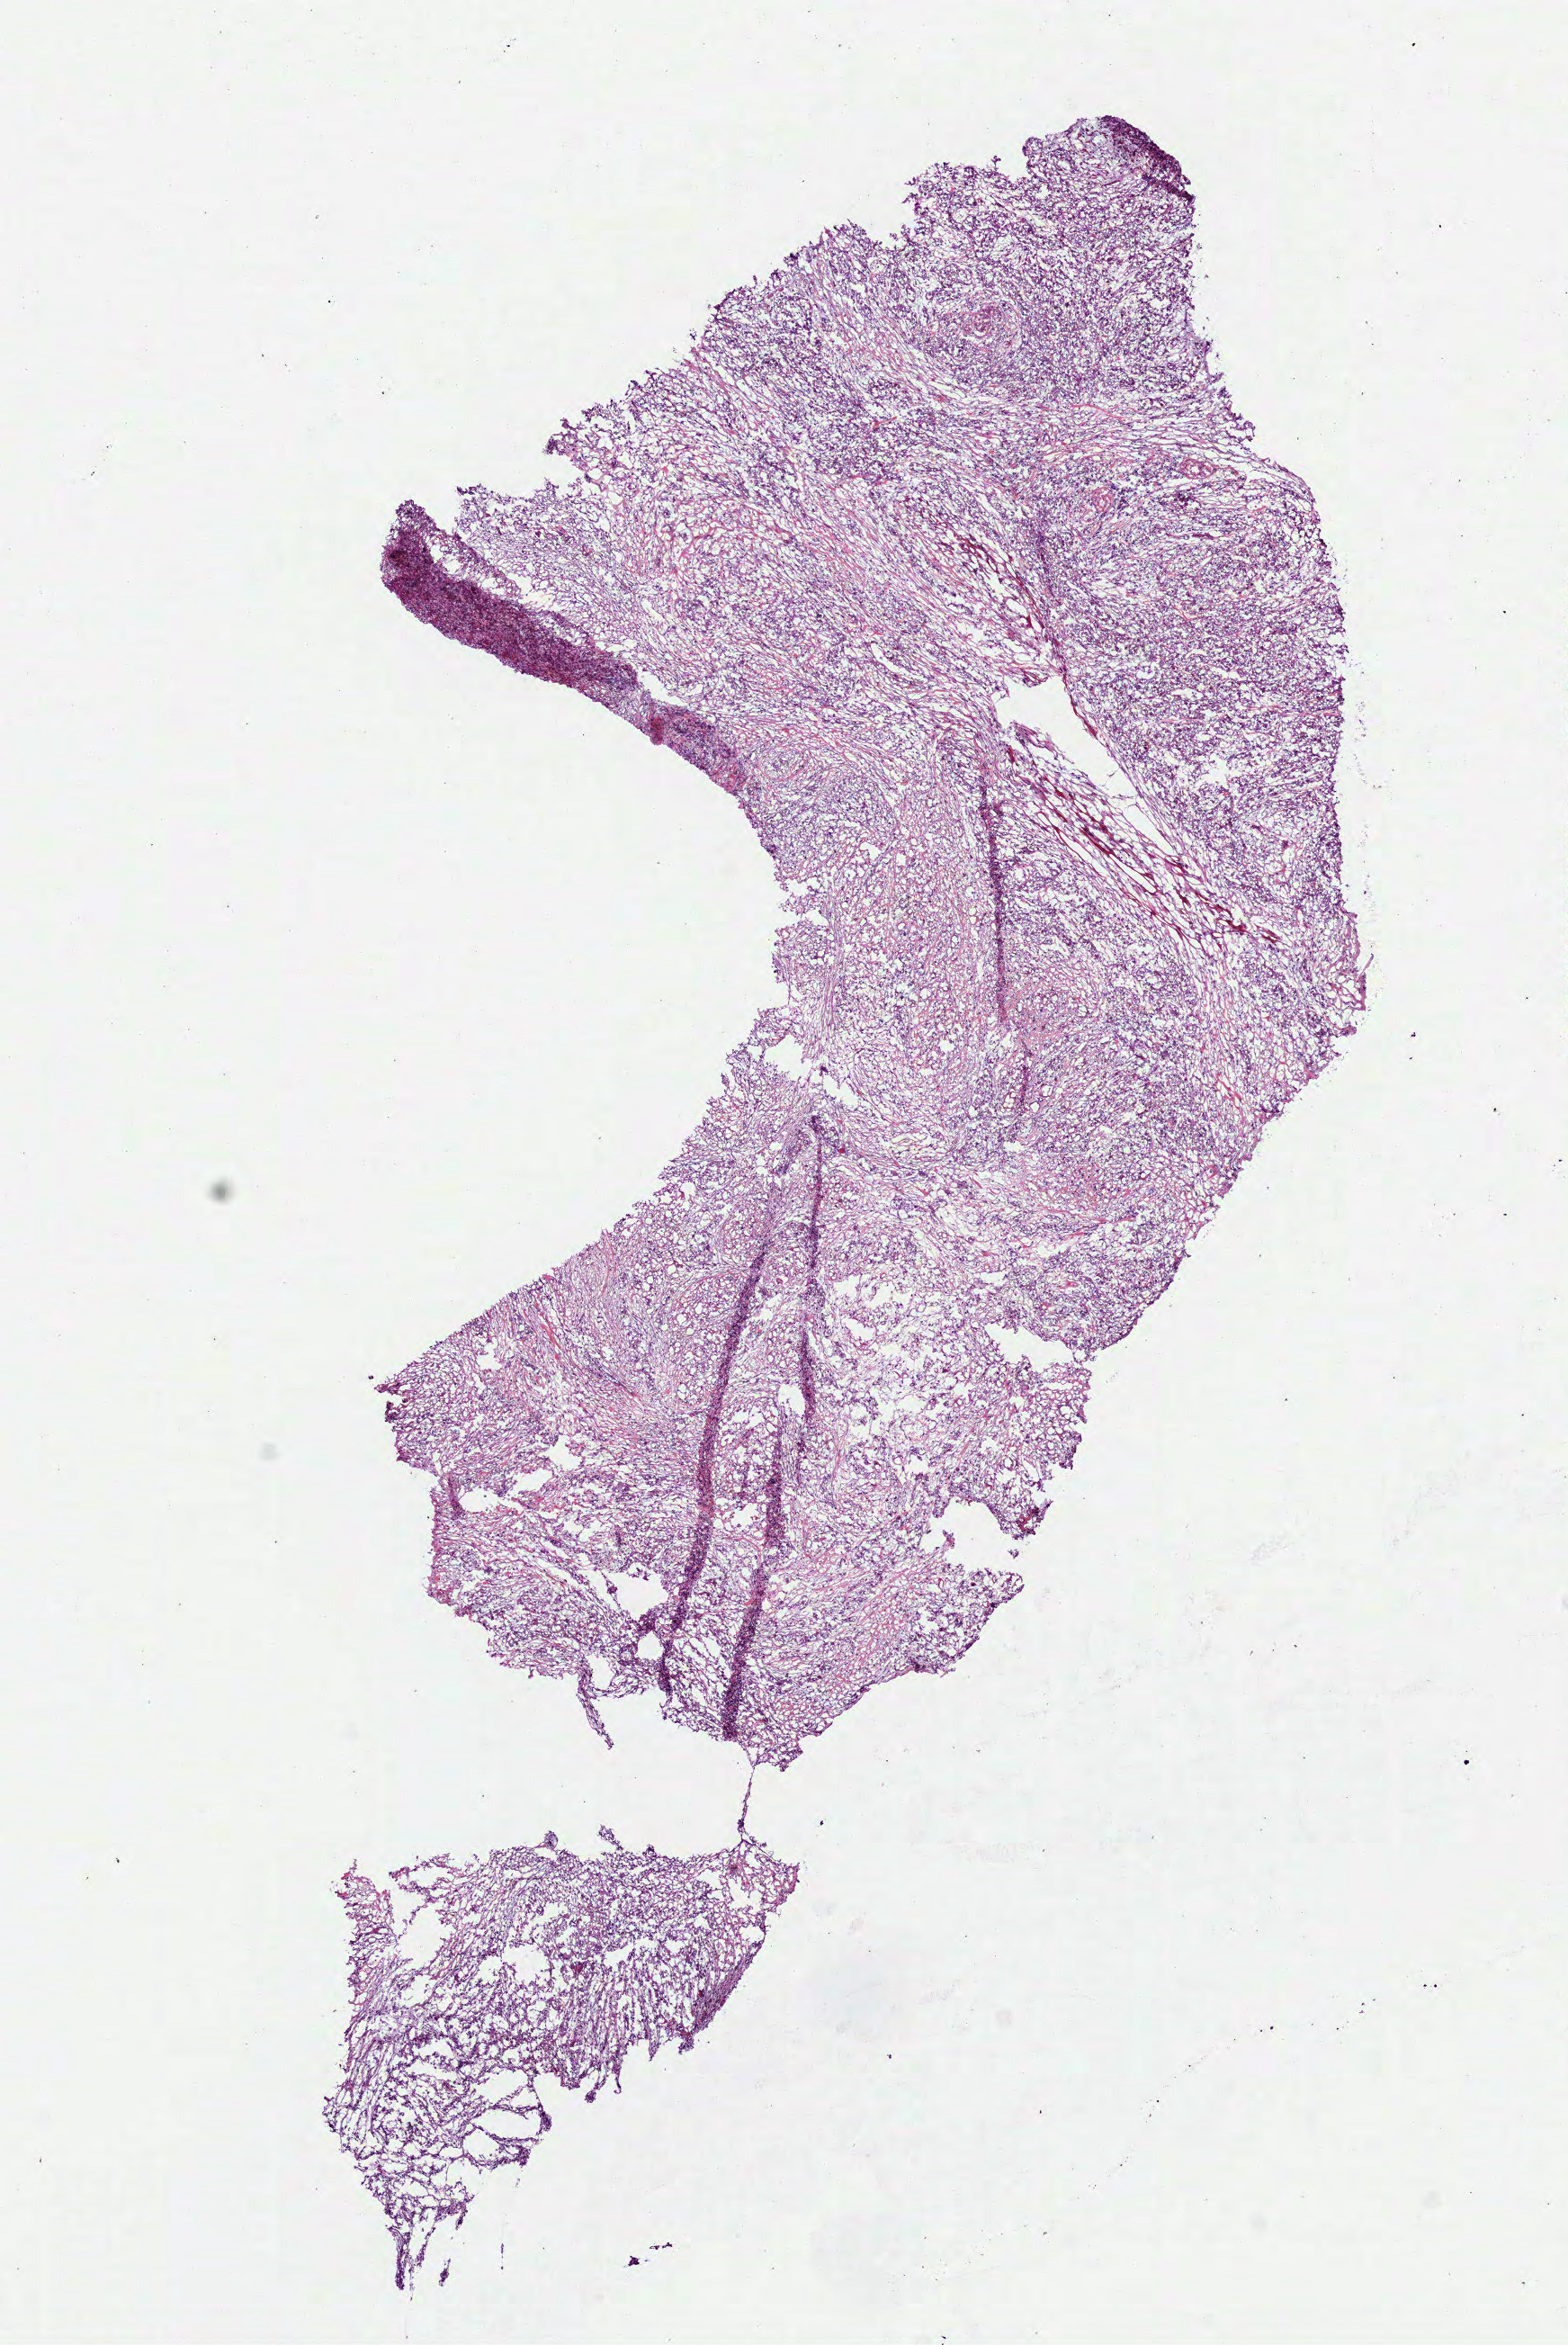
Whole-slide histology image, H&E-stained — low-resolution overview of the scanned area, about 7.0 x 10.5 mm (from a 40x scan). Frozen section from the bottom of the tissue portion. Primary tumour sample from the head and neck. Male, age 52 years at initial diagnosis. Histologic grade: G3 (poorly differentiated). Pathologist review of this section (percent, as recorded): tumour cells 85%, tumour nuclei 80%, normal cells 0%, stromal cells 15%, necrosis 0%.
Laterality: left. Pathologic diagnosis: Squamous cell carcinoma, NOS (tongue, NOS). AJCC pathologic stage: IVA (6th edition).